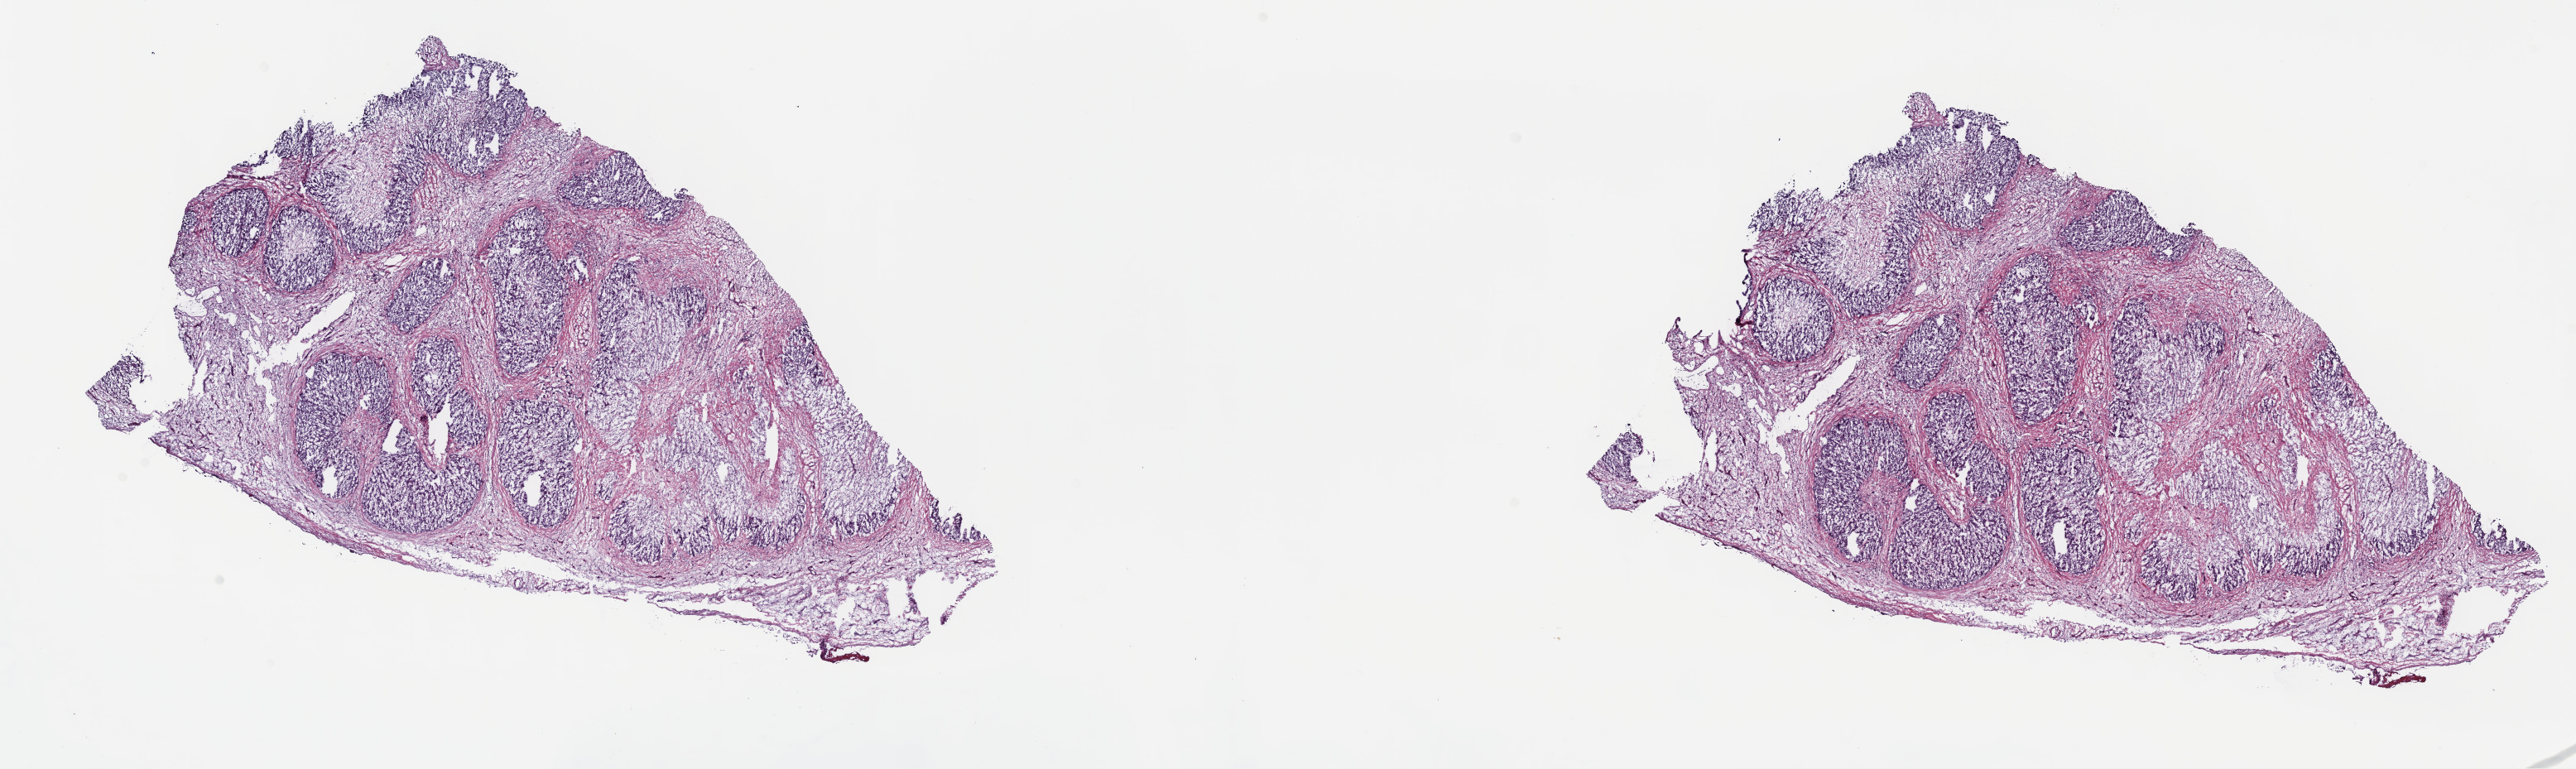
Digitized H&E-stained tissue section (whole slide), shown as a low-resolution overview of the whole scanned area (about 25.2 x 7.5 mm, acquisition: 40x scan); frozen section from the top of the tissue portion; liver, primary tumour sample. Male, age 58 years at initial diagnosis. Histologic grade: G2 (moderately differentiated). Pathologist review of this section (percent, as recorded): tumour cells 65%, tumour nuclei 65%, normal cells 0%, stromal cells 35%, necrosis 0%. Infiltration values recorded for this section: lymphocyte infiltration 4%, monocyte infiltration 2%, neutrophil infiltration 3%.
Histologic diagnosis: Hepatocellular carcinoma, NOS.